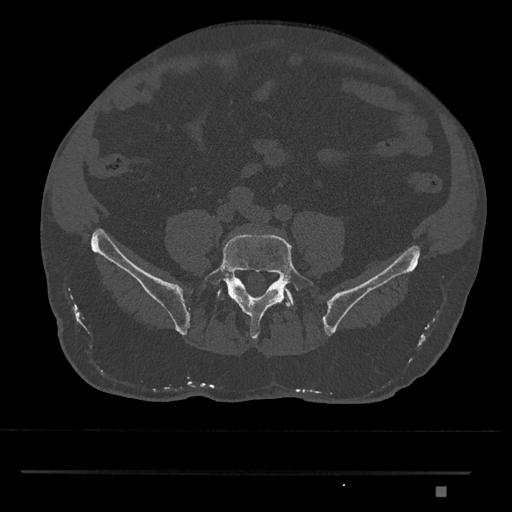
CT including the spine, one axial slice. Slice 557 of 1134 in the series (ordered by position). Reconstruction kernel Br40s/3. 120 kVp. Bone window (W 1800 / L 400 HU). 0.5 mm slice thickness. 512 × 512 image matrix. Patient: male, 65 years. From the clinical record (not read from this slice): primary cancer: prostate.
Annotated regions visible in this slice (semi-automatically segmented with operator editing):
- L5 vertebra: bounding box [x1, y1, x2, y2] px = [204, 234, 316, 340]